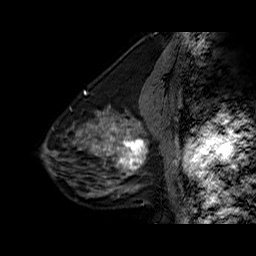
Breast MRI (dynamic contrast-enhanced), one sagittal slice; position 23 of 60 along the scan axis; dynamic contrast-enhanced series, time point 2 of 6 at this slice position (early post-contrast); 1.5 T; TE 6.3 ms, TR 32.5 ms; 256 × 256 image matrix. Female patient. From the clinical record (not read from this slice): setting: breast cancer imaged before/during neoadjuvant chemotherapy; receptor status: triple-negative.
Structures marked on this image (semi-automatically segmented with operator editing):
- analysis volume of interest (the breast-tissue region the enhancement analysis was run in; not a lesion): bounding box [x1, y1, x2, y2] px = [108, 126, 154, 177]
- tumour enhancement mask (voxels above the 100 % enhancement threshold inside the analysis volume of interest): [108, 126, 147, 170]